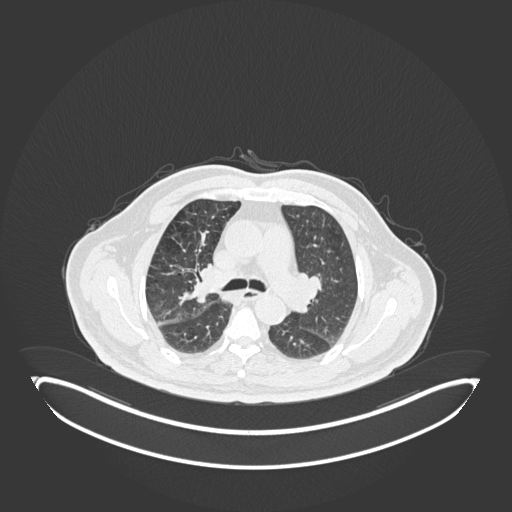
Chest CT, one axial slice. Position 115 of 247 along the scan axis. 120 kVp. Lung window (W 1500 / L -600 HU). 1 mm slice thickness. 512 × 512 image matrix, field of view 500 × 500 mm. Male patient, age 72 years. From the clinical record (not read from this slice): clinical TNM (as recorded): T1c N0 M0.
Structures marked on this image (rectangle marked by the reading radiologist):
- lung tumour (recorded histology: squamous cell carcinoma): bounding box (x1, y1, x2, y2) in pixels: (187, 264, 212, 307)